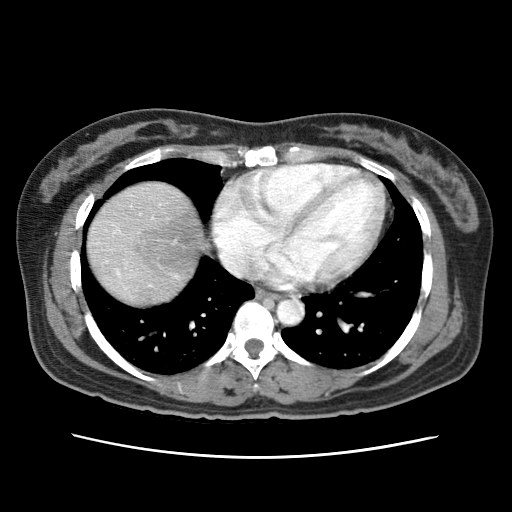
Contrast-enhanced abdominal CT (liver protocol), one axial slice; 120 kVp; soft-tissue window (W 400 / L 40 HU); 512 × 512 image matrix. From the clinical record (not read from this slice): diagnosis: hepatocellular carcinoma (patient treated with transarterial chemoembolisation; whether this scan precedes or follows treatment is not stated here); TNM stage (as recorded): Stage-I; Child-Pugh class: A; tumour differentiation: moderately differentiated; tumour nodularity: uninodular.
Structures marked on this image (semi-automatically segmented with operator editing):
- abdominal aorta: box from (x=276, y=298) to (x=303, y=326) px
- liver parenchyma outside the tumour (the mass and vessels are separate outlines, so this box may not span the whole liver): (x=88, y=182)–(x=201, y=304)
- liver vessels: (x=117, y=272)–(x=120, y=275)